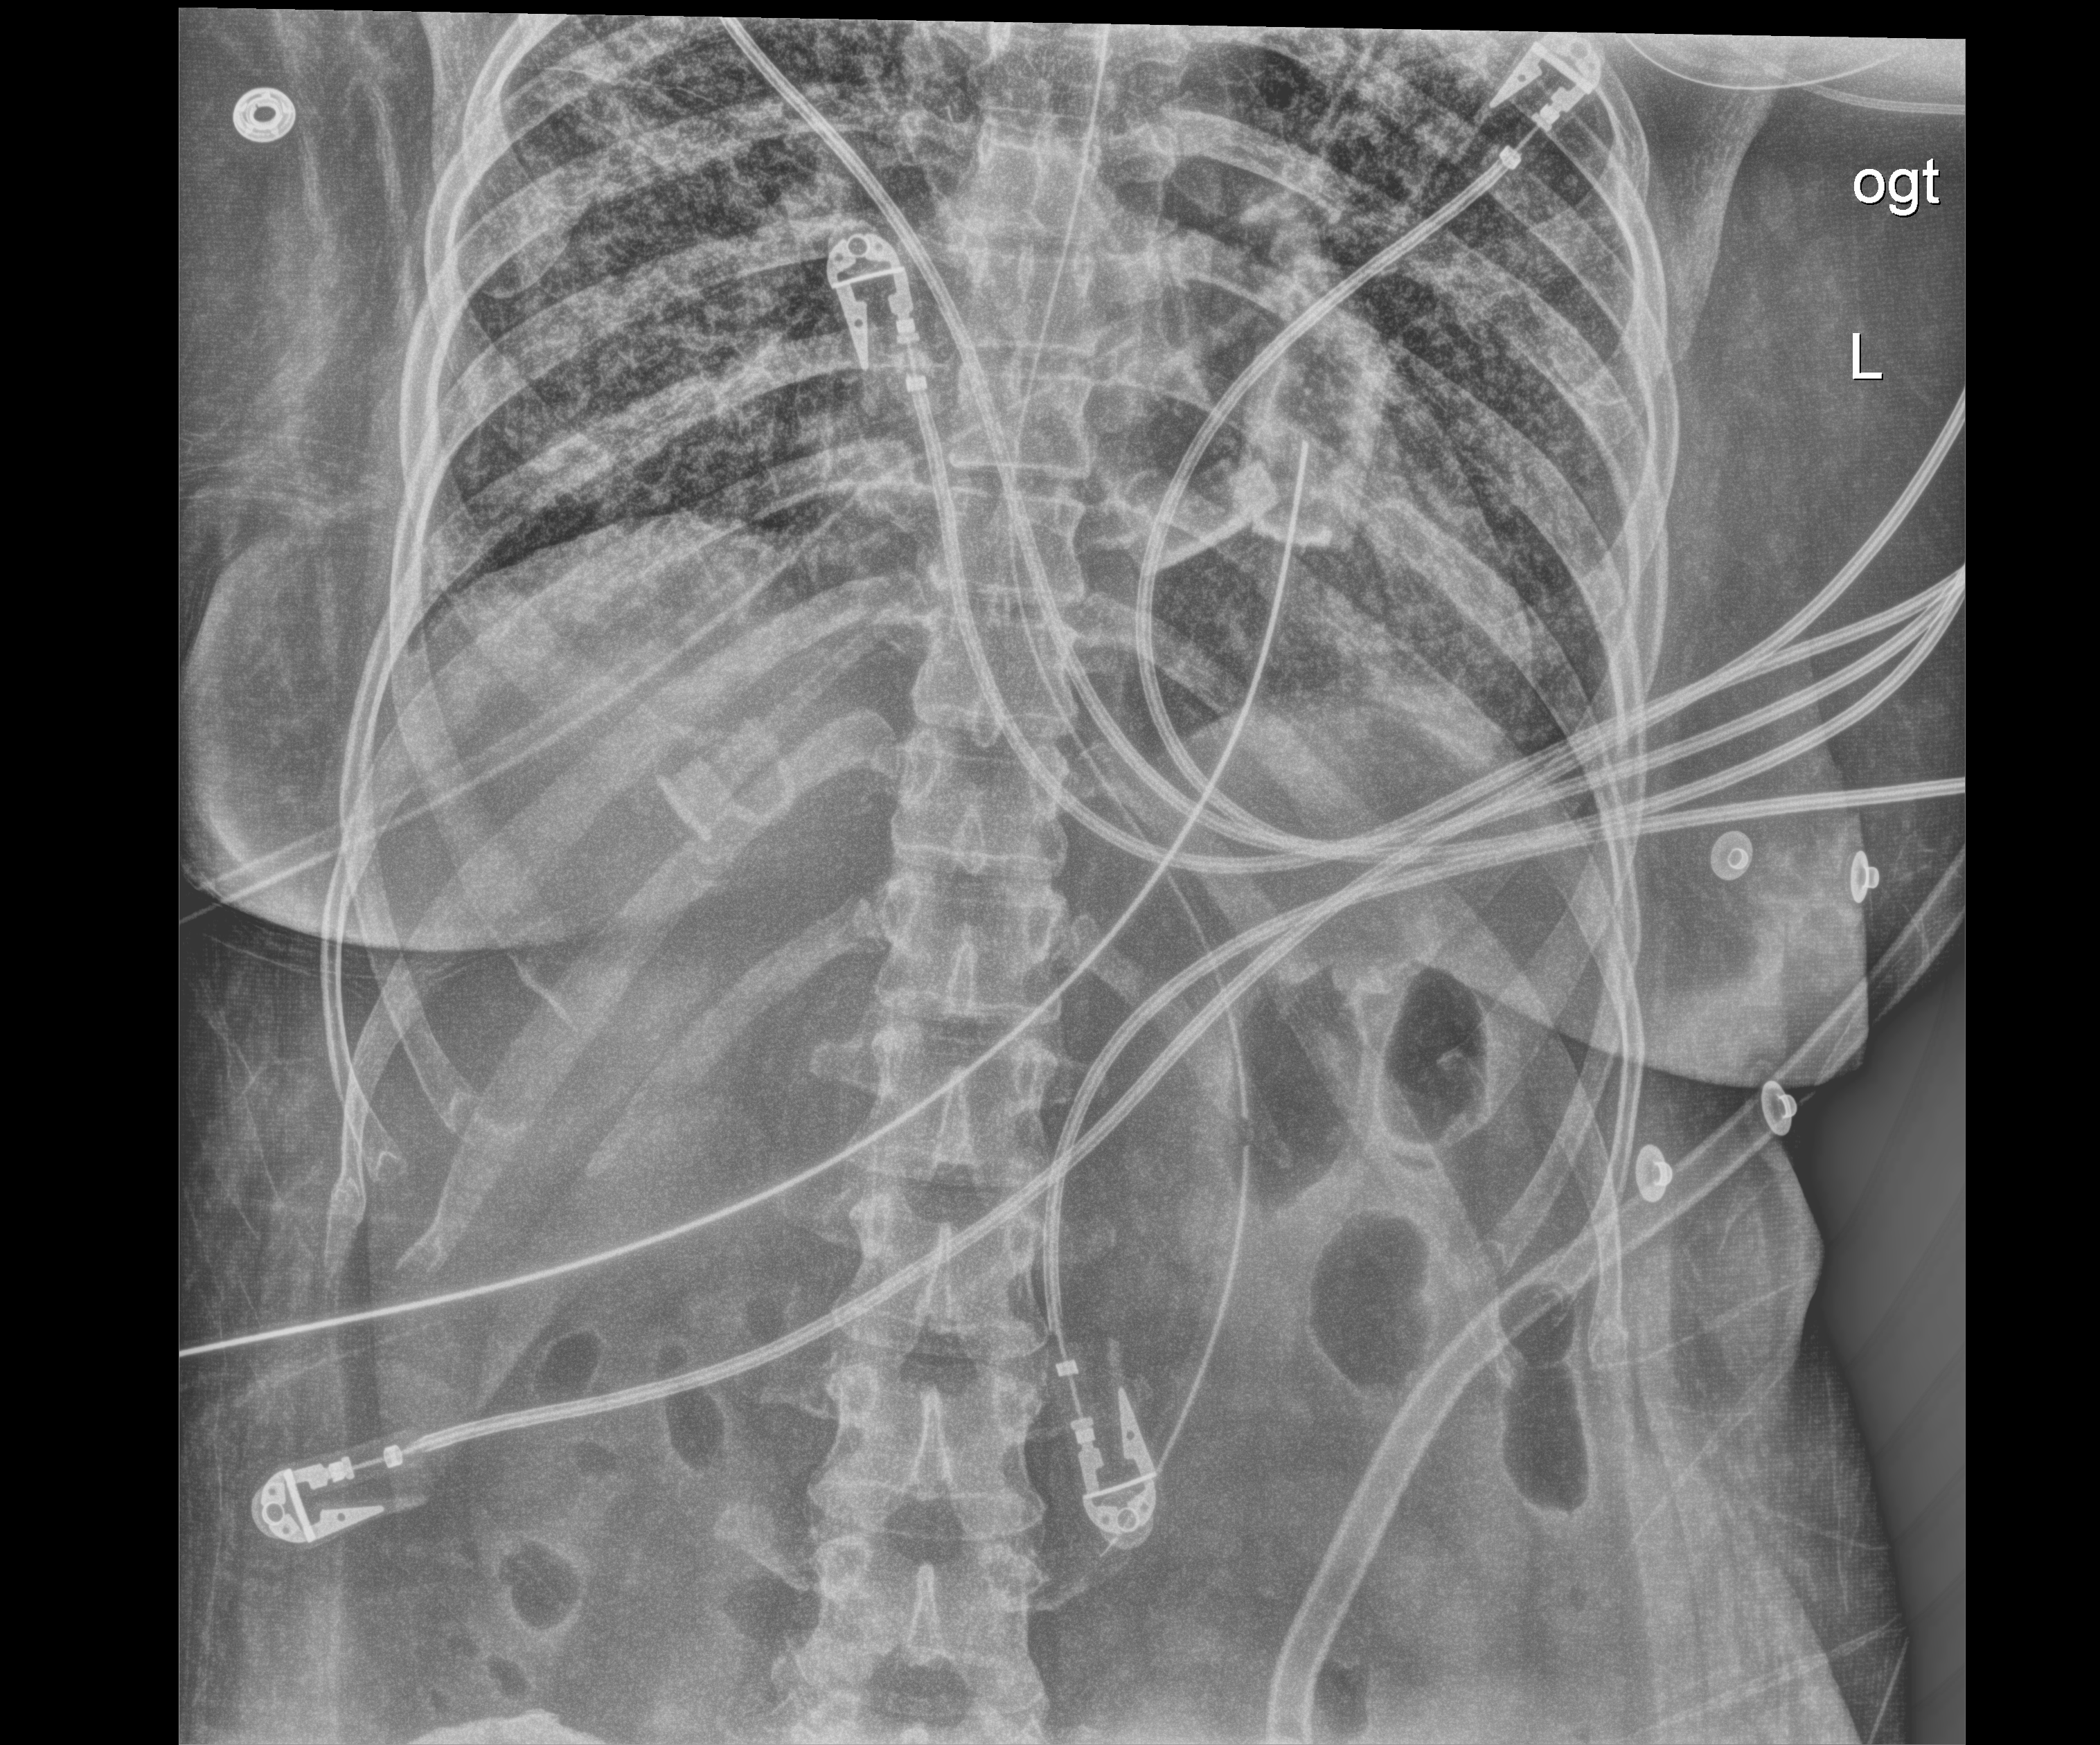
Bedside chest radiograph (digital radiography), anteroposterior (AP) projection. Patient hospitalised with COVID-19; male, aged 18–59 years.
Hospital-stay facts (about this admission, not read from this image; timing relative to this image not recorded):
- admitted to intensive care during this hospital stay: yes
- mechanically ventilated during this hospital stay: yes